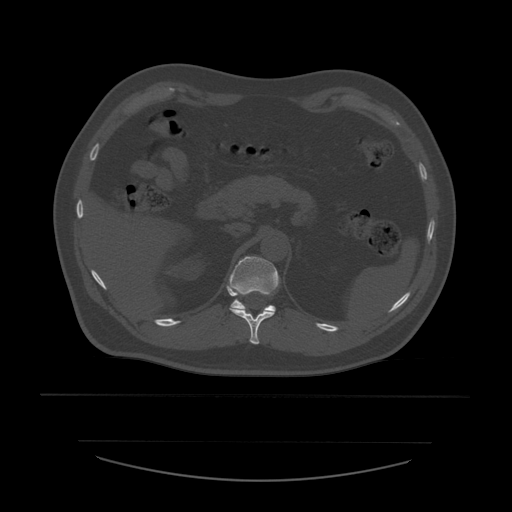
CT including the spine, one axial slice. Slice 264 of 532 in the series (ordered by position). Reconstruction kernel STANDARD. 120 kVp. Bone window (W 1800 / L 400 HU). 1.25 mm slice thickness. 512 × 512 image matrix. Patient age 44 years. Case-level facts recorded for this patient, not image findings: primary cancer: soft tissue sarcoma.
Annotated regions visible in this slice (semi-automatic segmentation, software-assisted and operator-edited):
- T11 vertebra: bounding box (x1, y1, x2, y2) in pixels: (230, 291, 275, 345)
- T12 vertebra: (227, 256, 280, 312)